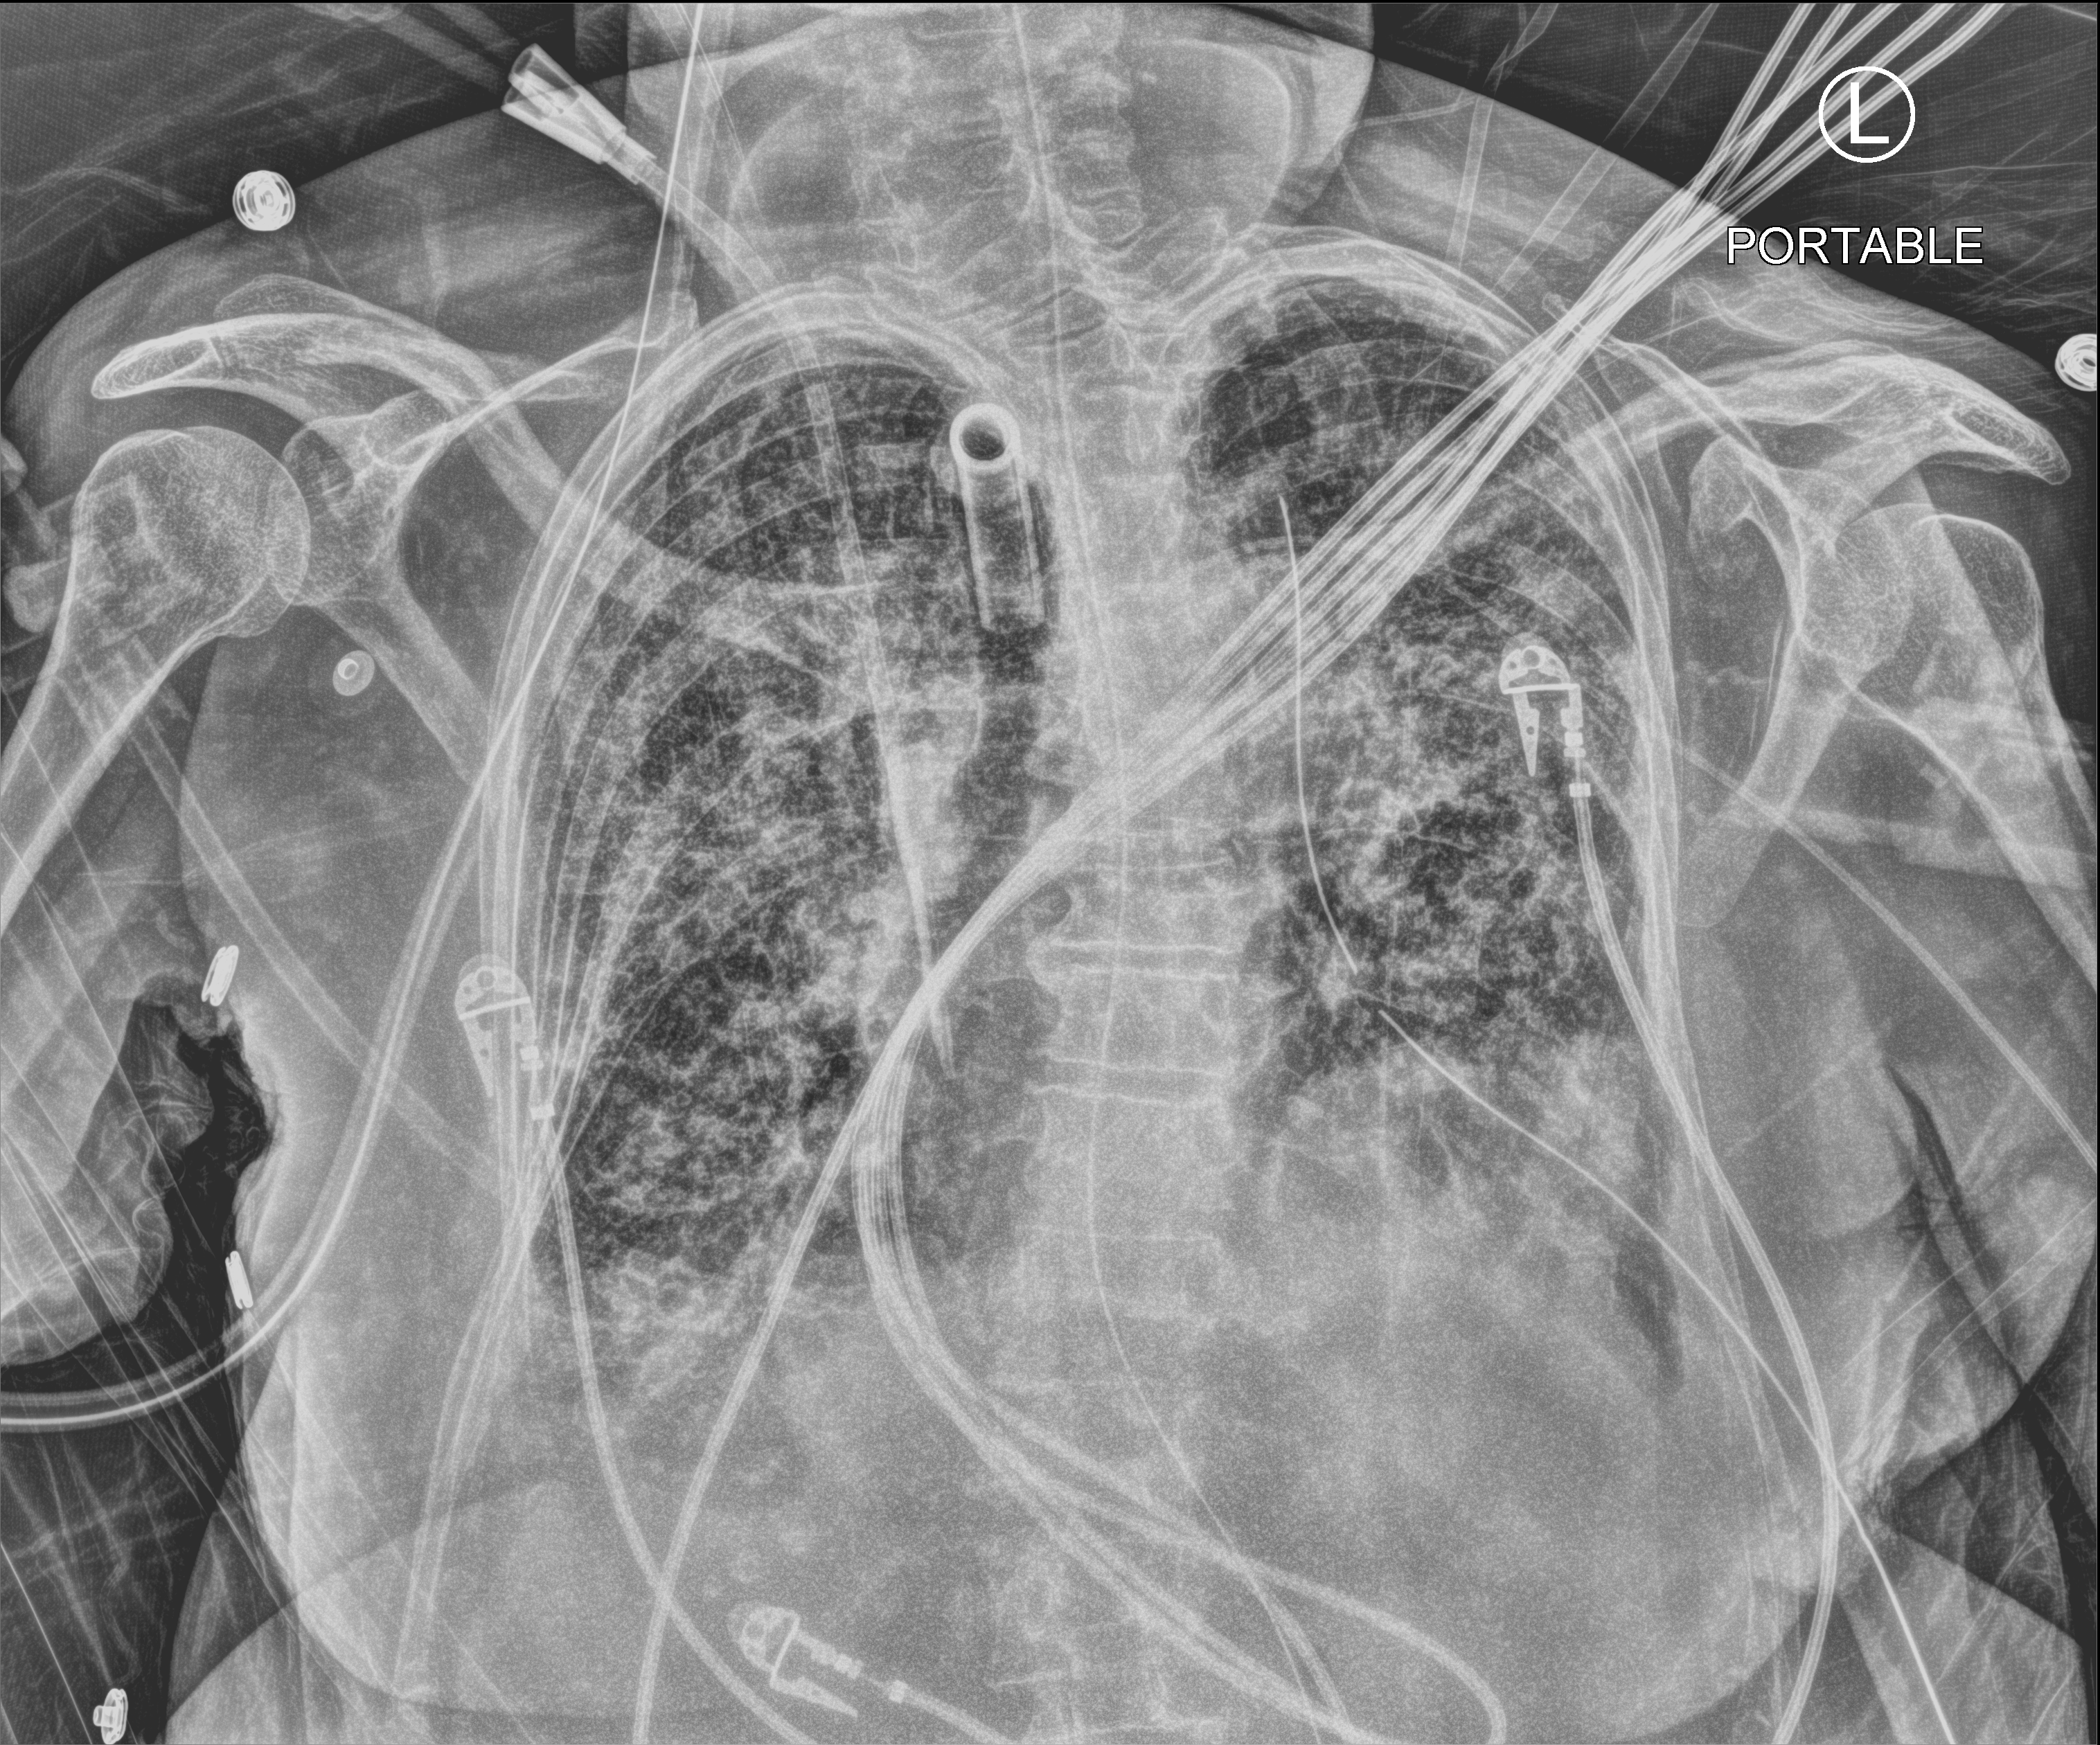
Bedside chest radiograph (computed radiography); anteroposterior (AP) projection. Female patient hospitalised with COVID-19, age 75–90 years.
Hospital-stay facts (about this admission, not read from this image; timing relative to this image not recorded): smoking status (admission record): former; length of hospital stay: 70 days; admitted to intensive care during this hospital stay: yes.